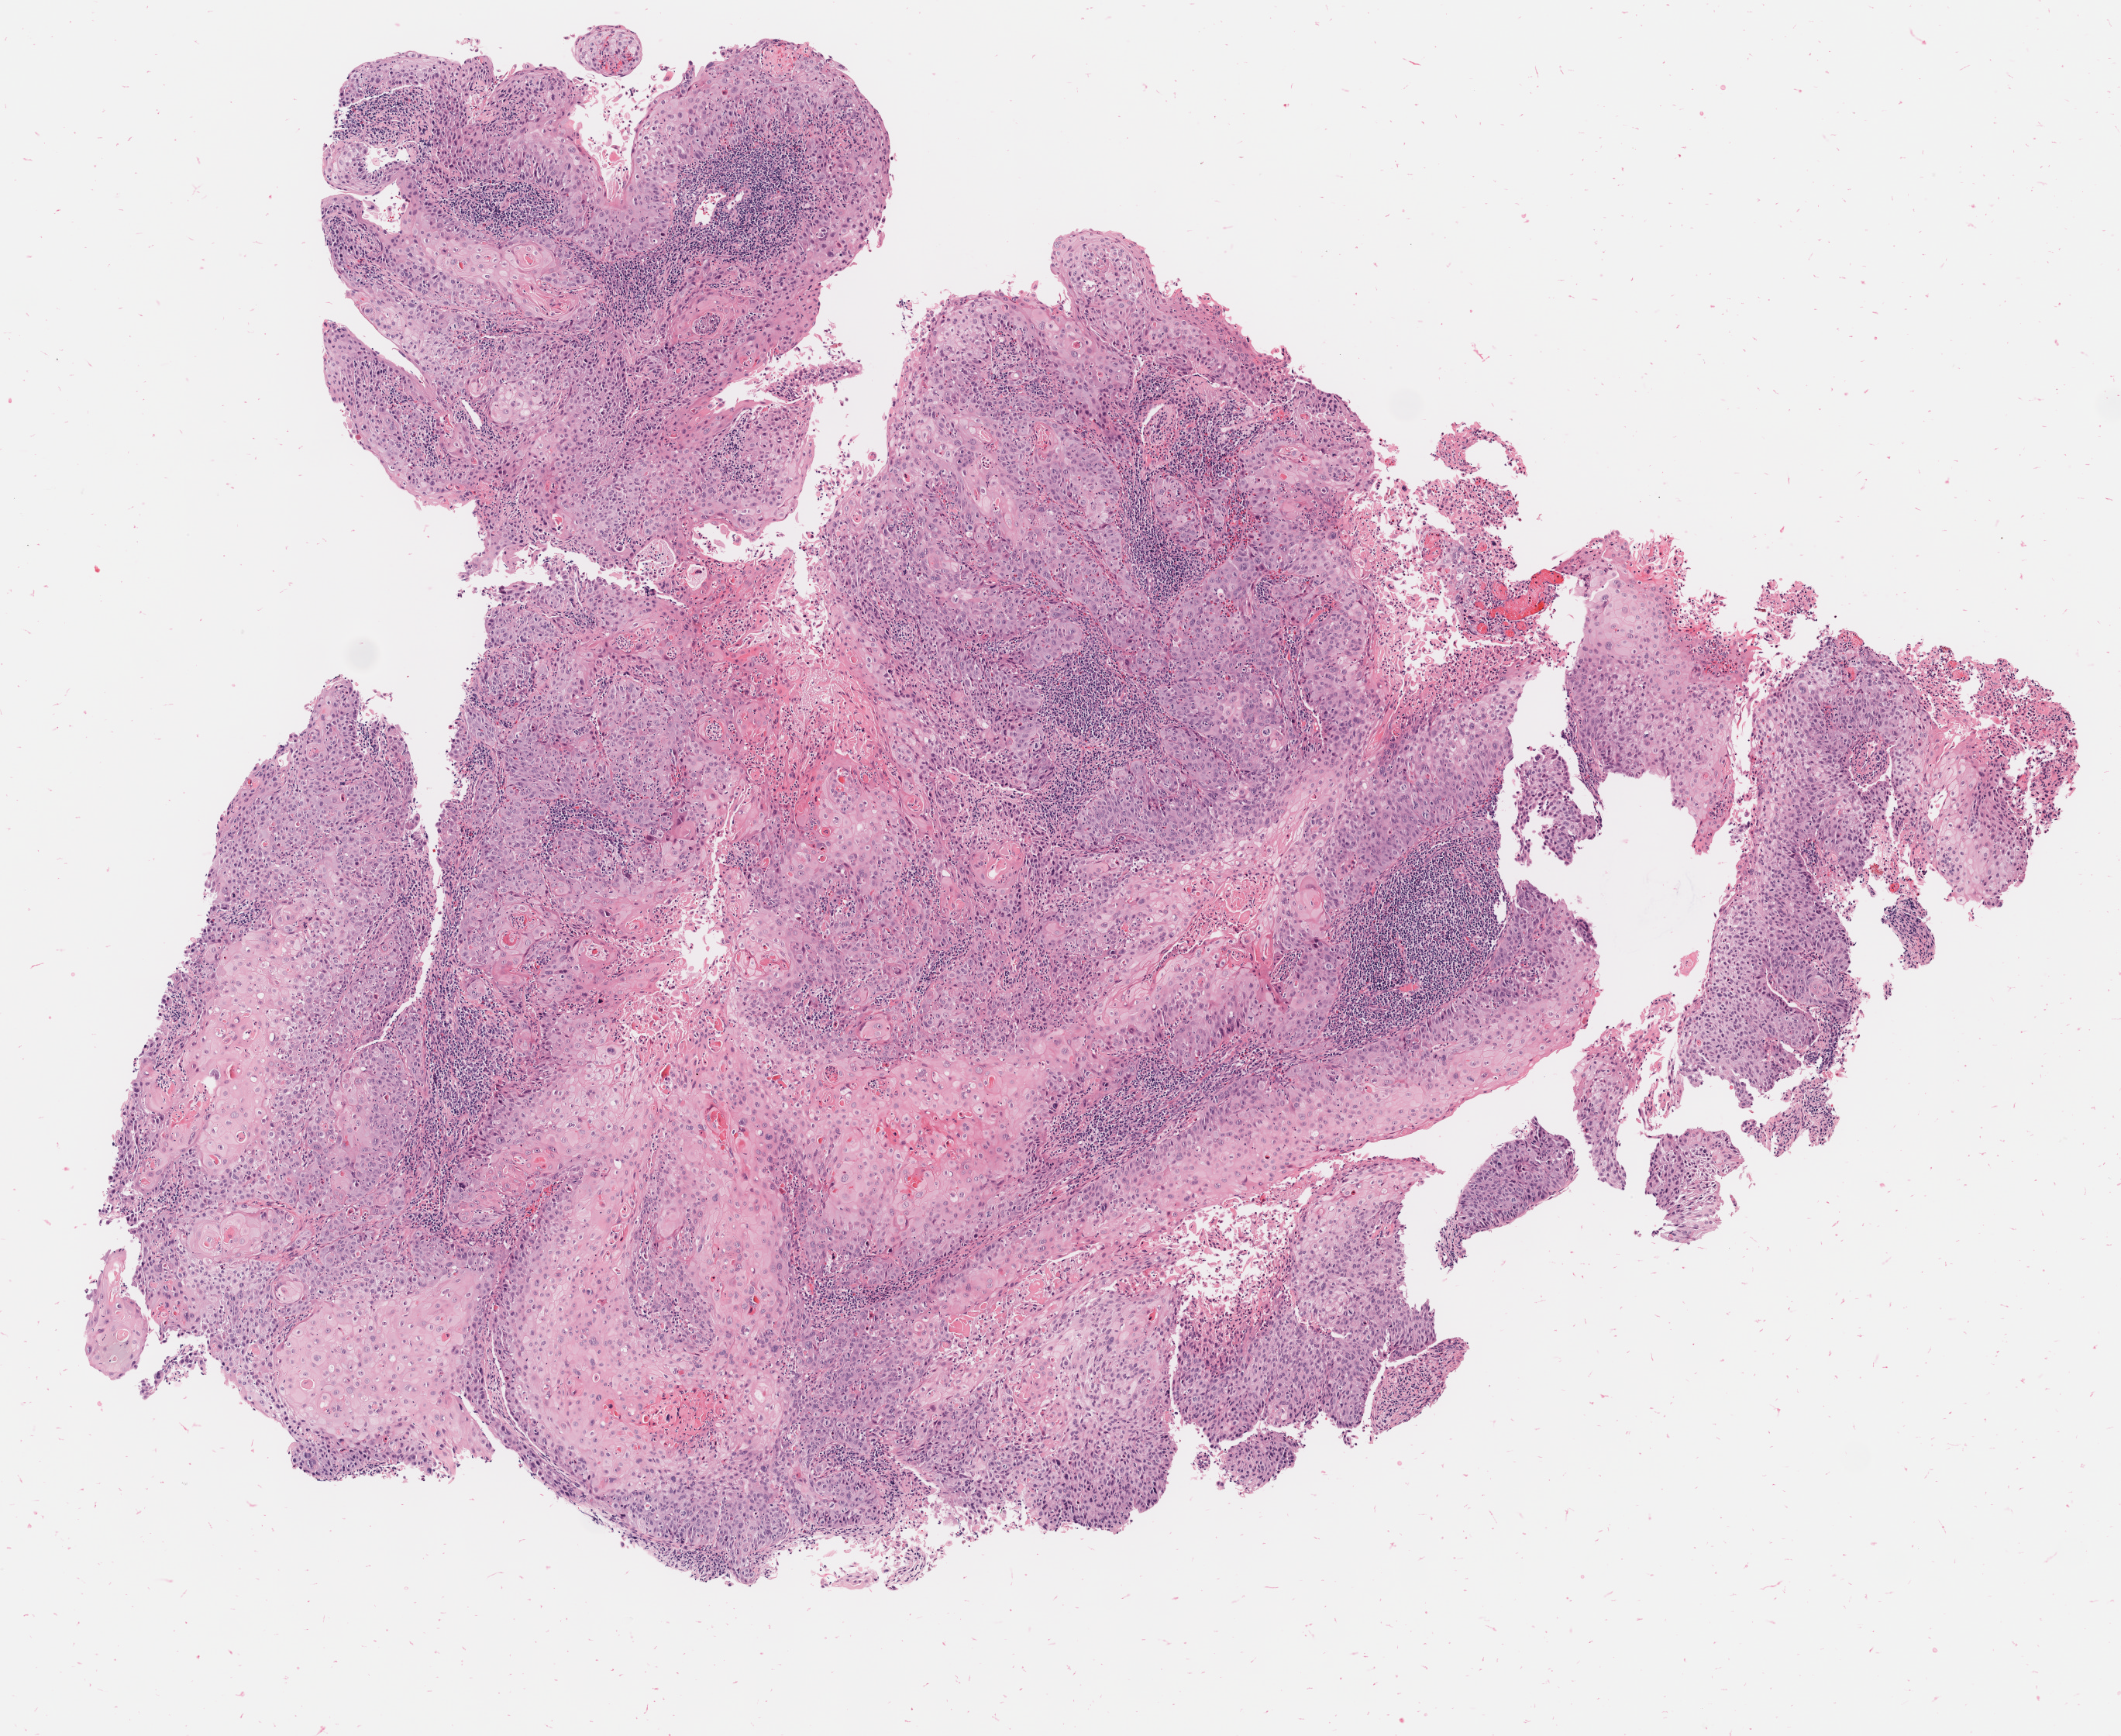
H&E whole-slide image, a low-resolution overview of the entire scanned area, about 5.4 x 4.5 mm; specimen: tumor tissue; site: cervix. Patient female; 31 years old.
* histologic diagnosis: Squamous cell carcinoma, keratinizing, NOS